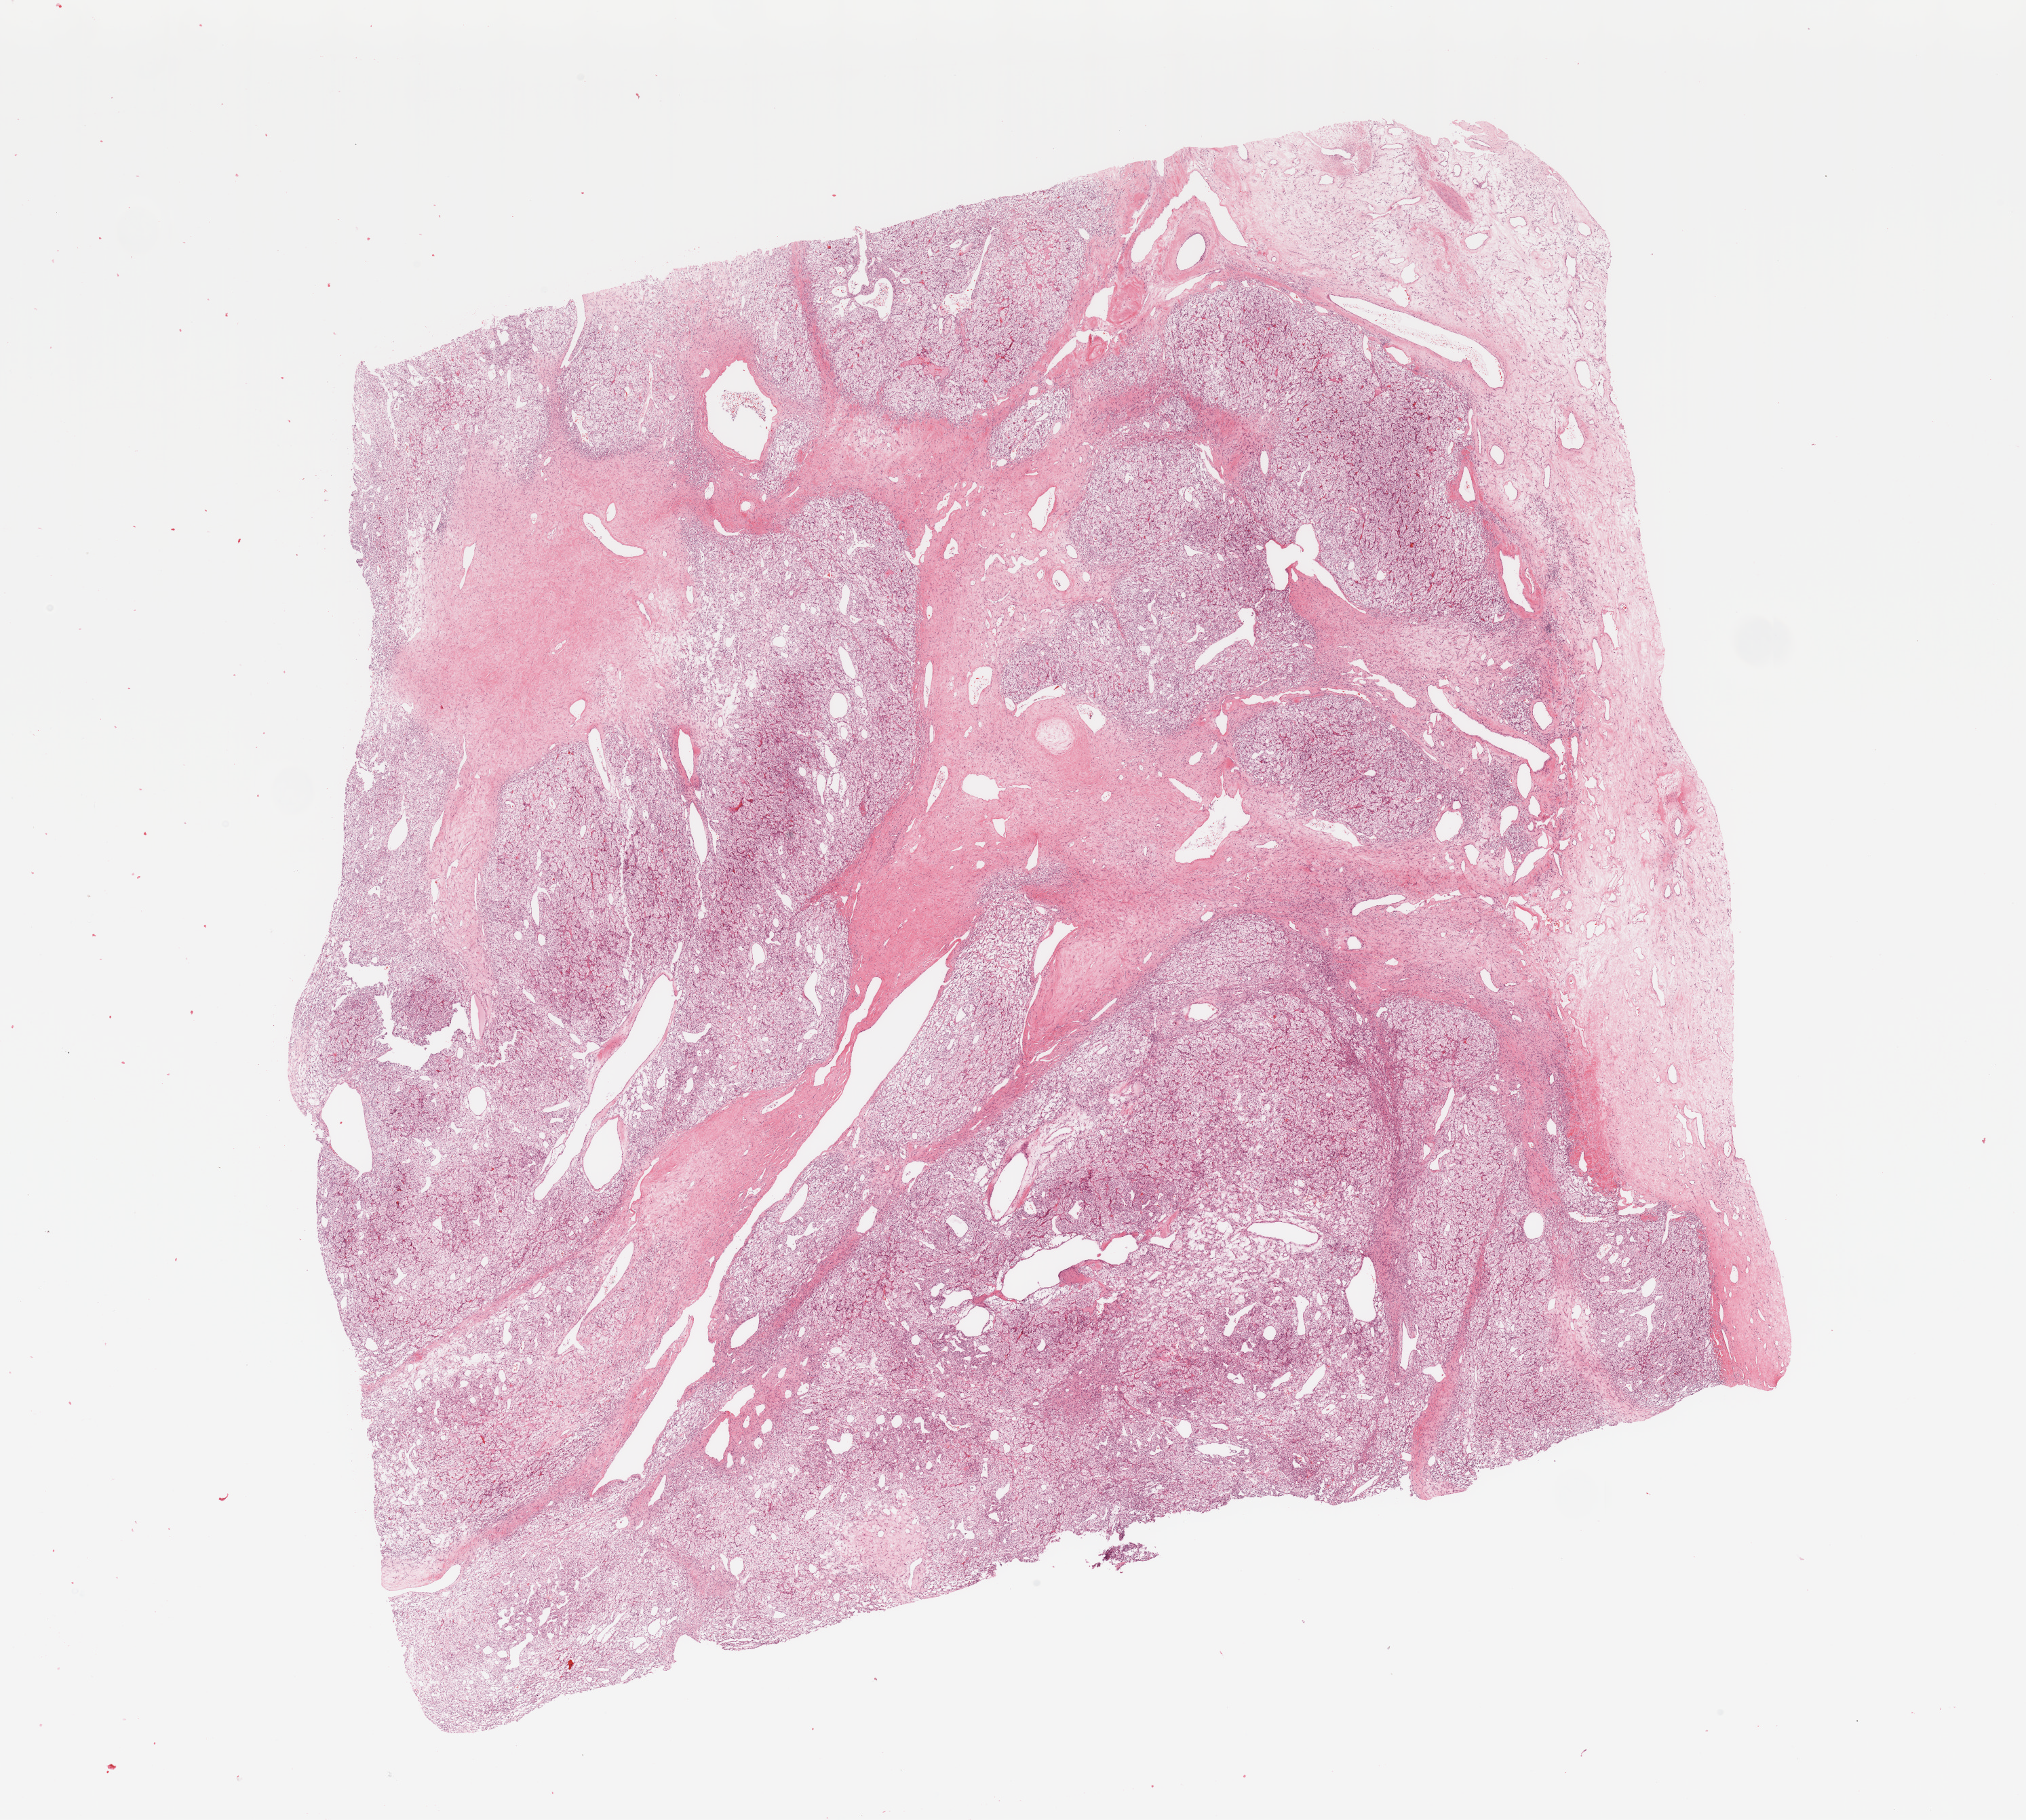
Whole-slide histology image, H&E-stained — a low-resolution overview of the entire scanned area, about 23.6 x 21.2 mm (acquisition: 20x scan); tumour tissue sample, kidney. 57-year-old female patient. Histologic grade: G1 (well differentiated).
Histologic diagnosis: Renal cell carcinoma, NOS.